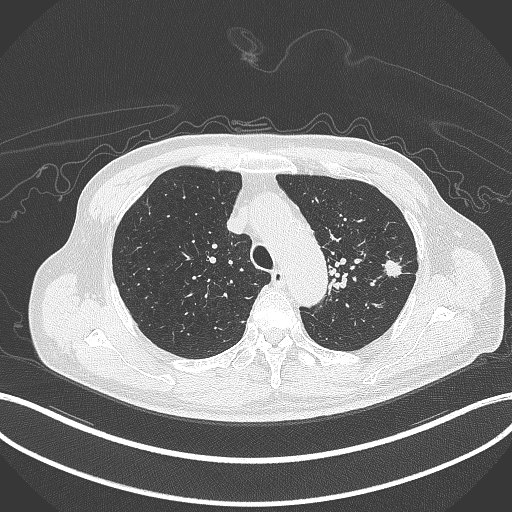
Chest CT, one axial slice. Slice 335 of 417 in the series (ordered by position). Reconstruction kernel B70f. Lung window (W 1500 / L -600 HU). 1 mm slice thickness. 512 × 512 image matrix, field of view 400 × 400 mm. Patient: male, 77 years. From the clinical record (not read from this slice): clinical TNM (as recorded): T3 N1 M0.
Outlined on this slice (bounding box drawn by a radiologist):
- lung tumour (recorded histology: adenocarcinoma): bounding box [x1, y1, x2, y2] px = [380, 255, 405, 281]